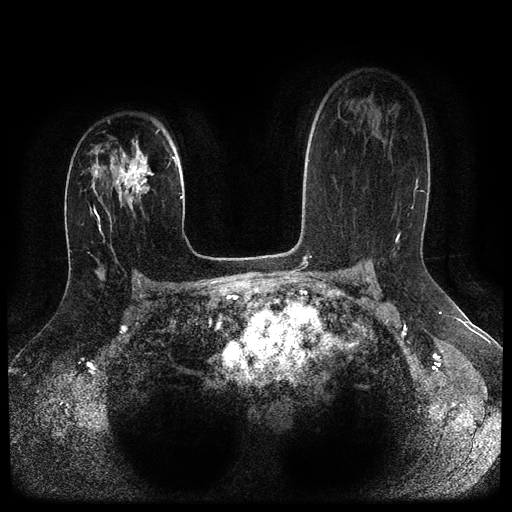
Breast MRI (dynamic contrast-enhanced, multi-phase), one axial slice; position 67 of 116 along the scan axis; dynamic contrast-enhanced series, time point 2 of 5 at this slice position (early post-contrast); 1.5 T; TE 2.6 ms, TR 5.4 ms; 512 × 512 image matrix, field of view 340 × 340 mm. Female patient, age 29 years.
Outlined on this slice (semi-automatically segmented with operator editing):
- breast lesion (labelled 'tumour' in the annotation; benign lesions carry a separate 'benign' label): bounding box <107,140,155,210> (left, top, right, bottom; pixels)